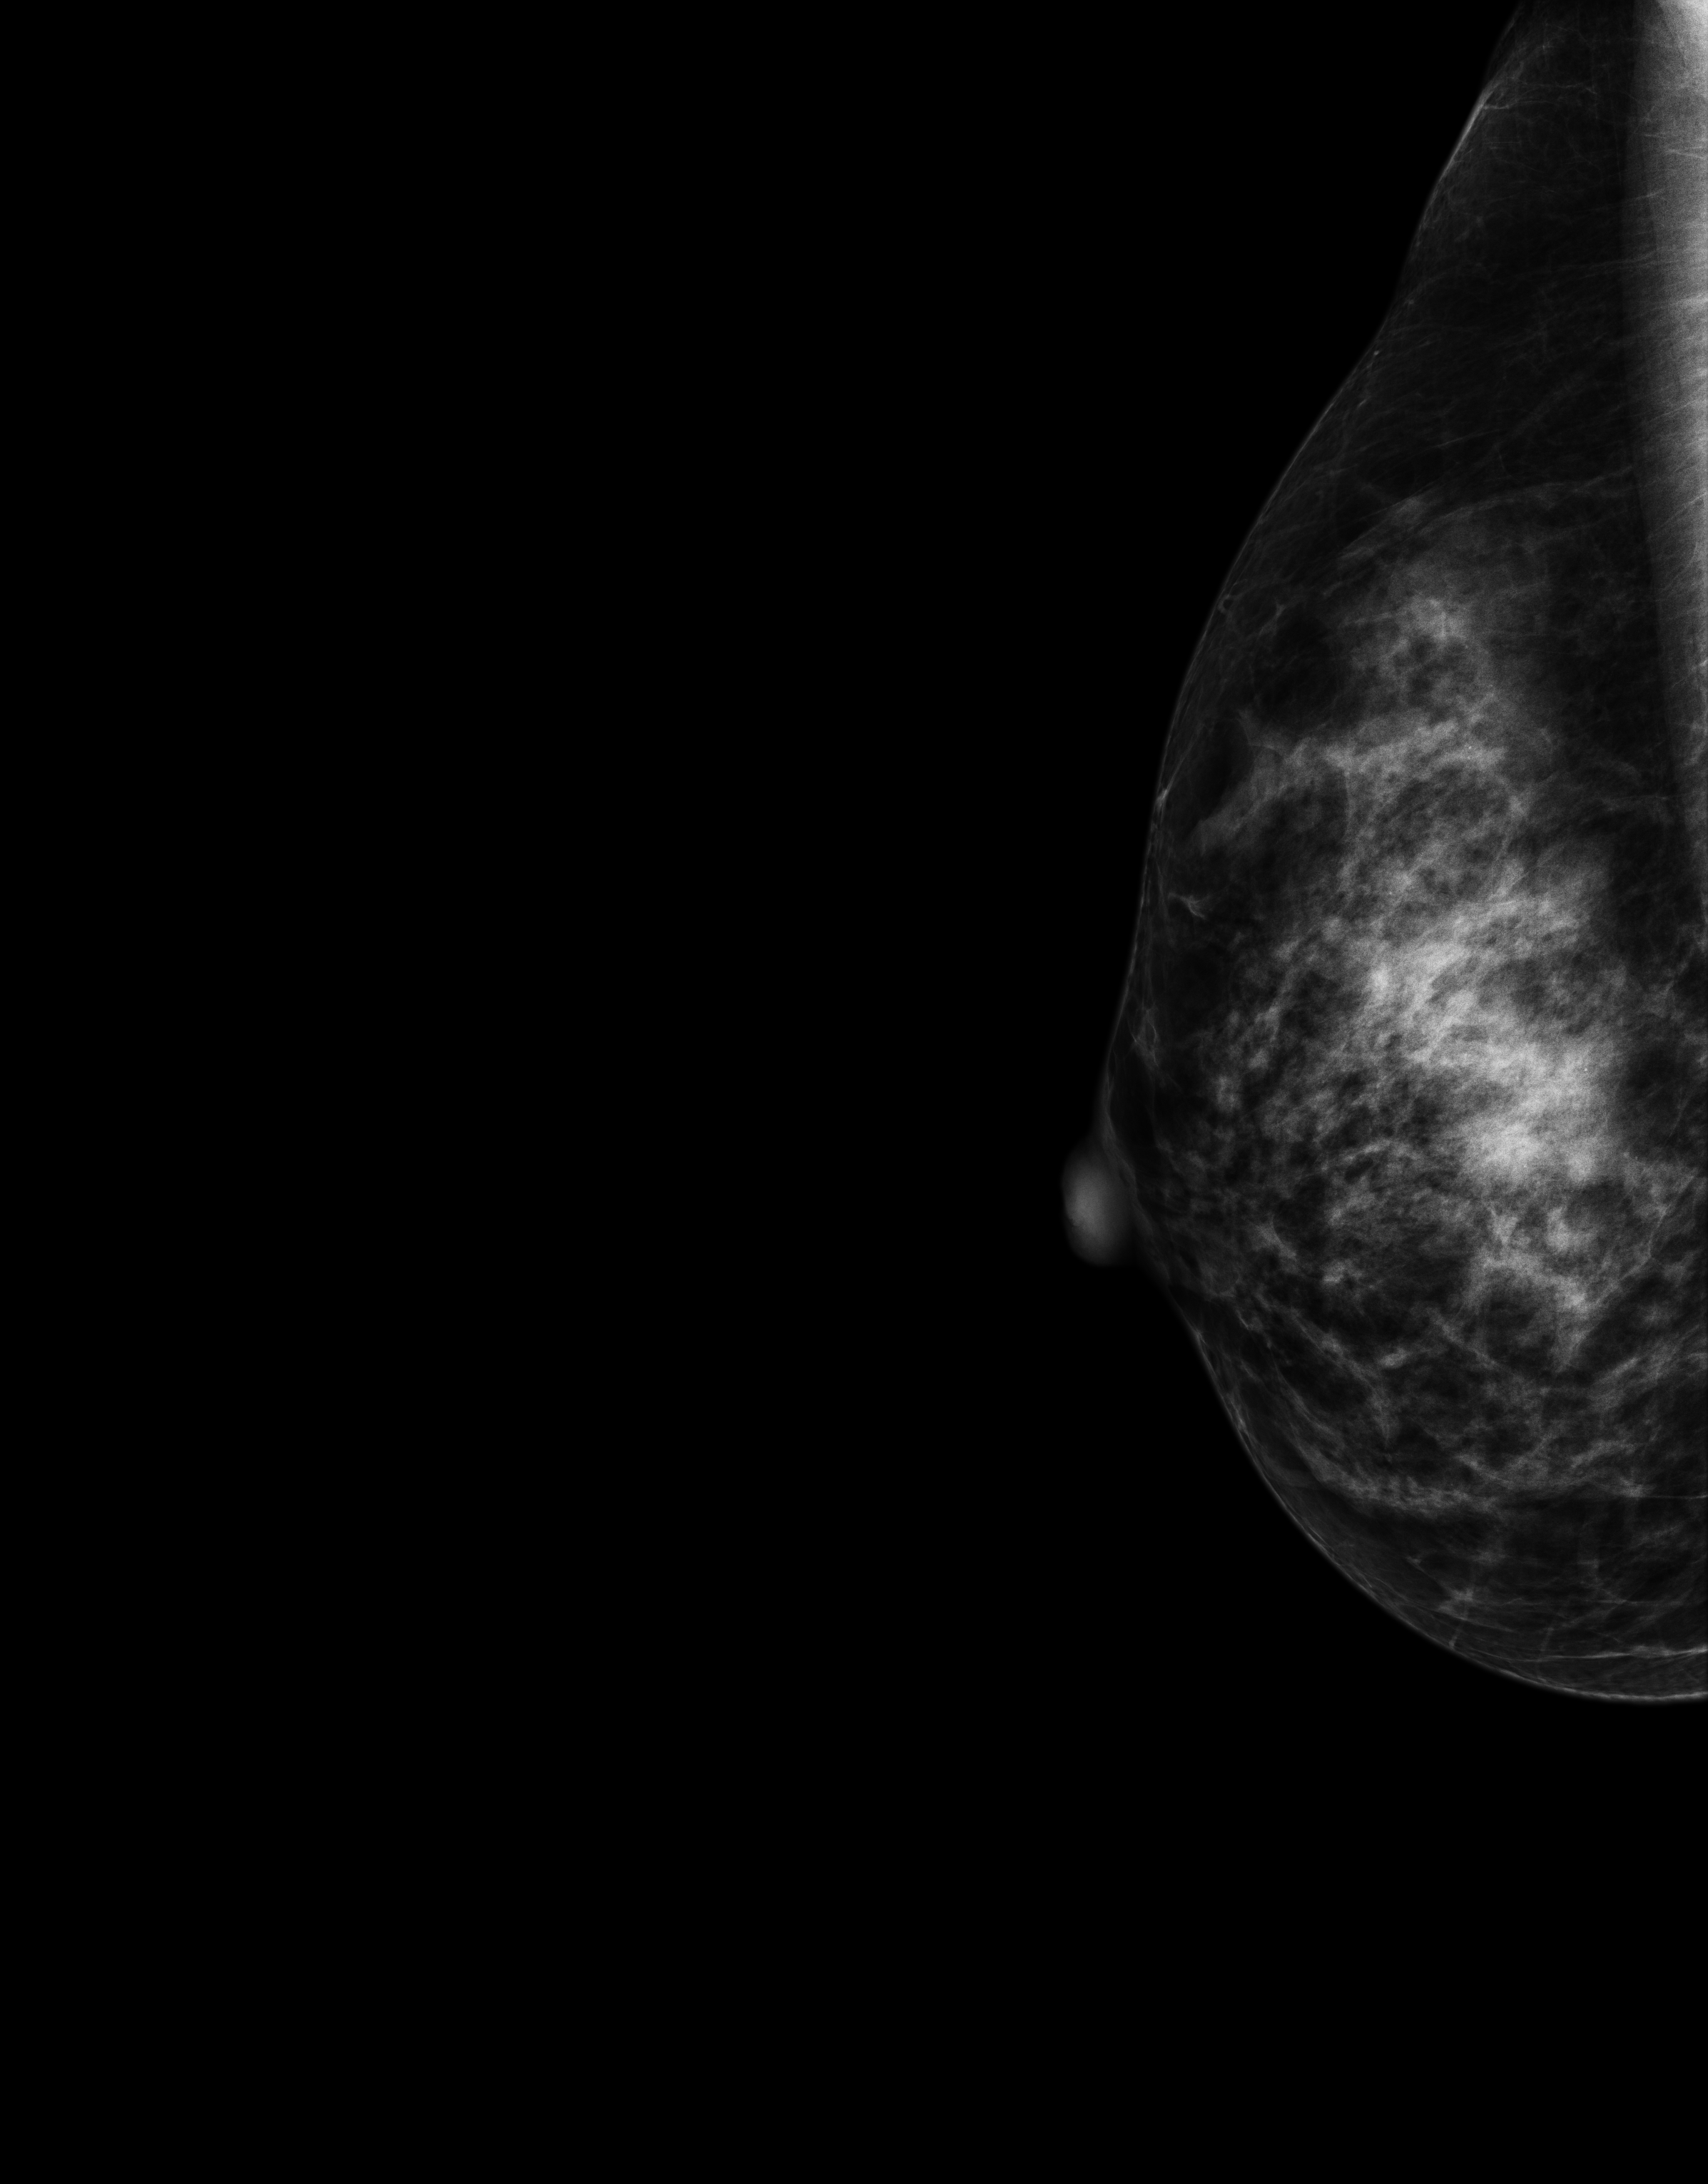
Screening examination. Patient: female, 43 years.
Image type: full-field digital mammogram. Breast: right. Projection: laterally exaggerated craniocaudal (XCCL) view.